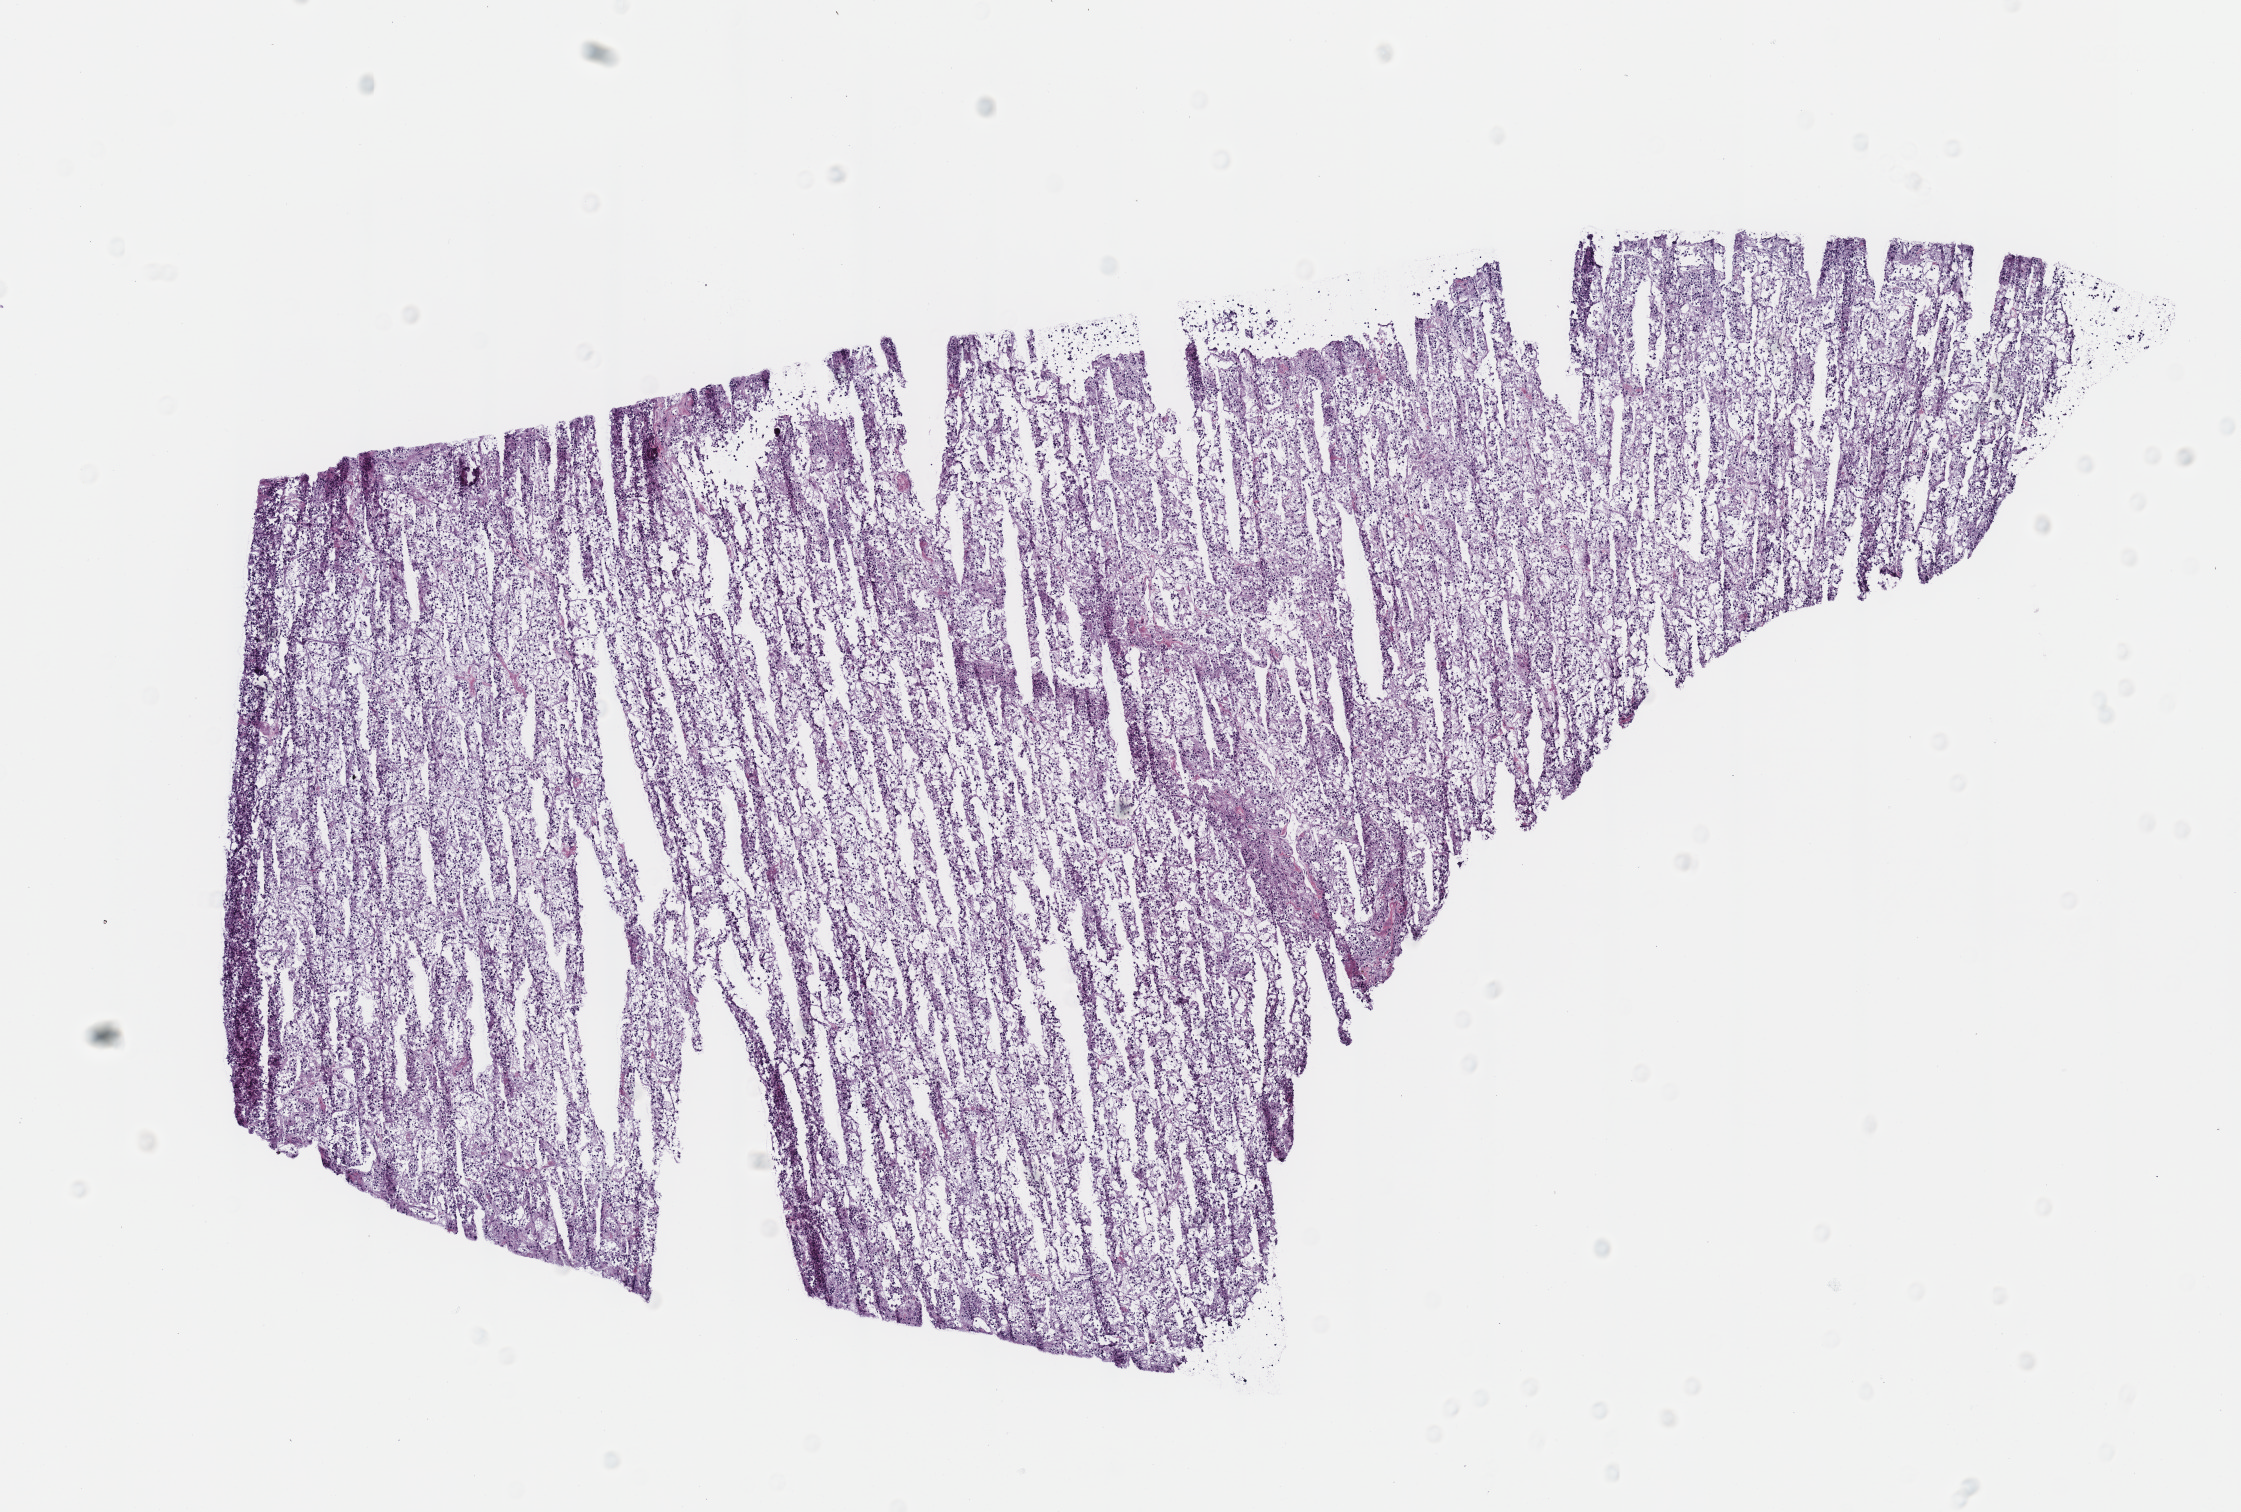
Hematoxylin and eosin (H&E) stained whole-slide image, low-resolution overview of the scanned area, about 8.8 x 5.9 mm (from a 40x scan). Frozen section from the top of the tissue portion. Sample: primary tumour, kidney. Patient: female, age at initial diagnosis 38 years. Histologic grade: G2 (moderately differentiated). Slide review estimates, as recorded: tumour cells 95%, tumour nuclei 90%, normal cells 0%, stromal cells 5%, necrosis 0%.
AJCC pathologic stage: I. Pathologic diagnosis: Clear cell adenocarcinoma, NOS.